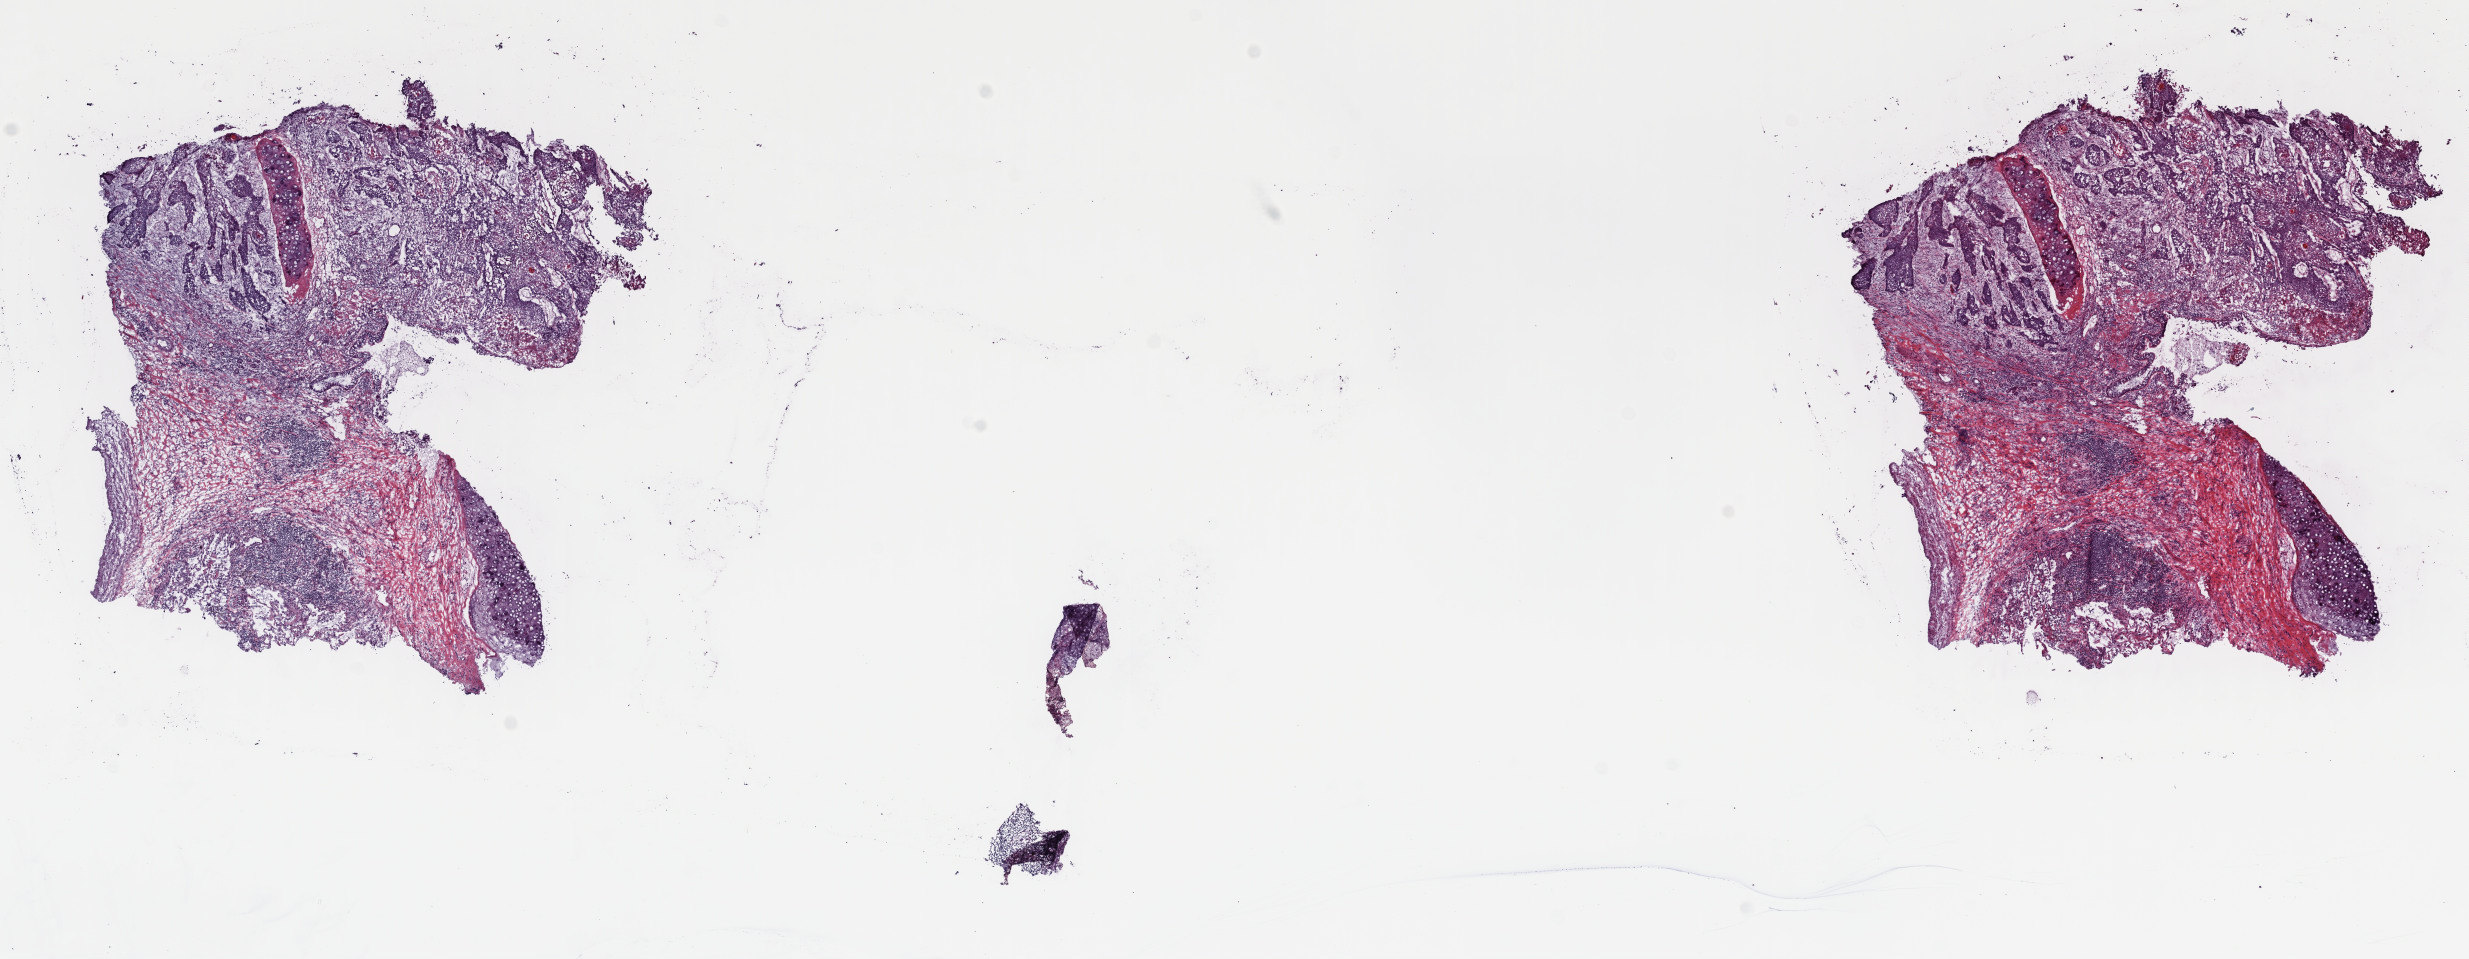
Digitized H&E-stained tissue section (whole slide), a low-resolution overview of the entire scanned area, about 19.5 x 7.6 mm (from a 40x scan). Frozen section from the top of the tissue portion. Sample: primary tumour, lung. Female, age 76 years at initial diagnosis. Slide review estimates, as recorded: tumour cells 30%, tumour nuclei 80%, normal cells 20%, stromal cells 50%, necrosis 0%. Inflammatory infiltration, as recorded: lymphocyte infiltration 8%, monocyte infiltration 6%, neutrophil infiltration 0%.
* pathologic diagnosis: Squamous cell carcinoma, NOS (upper lobe, lung)
* AJCC pathologic stage: IA (7th edition)
* laterality: right